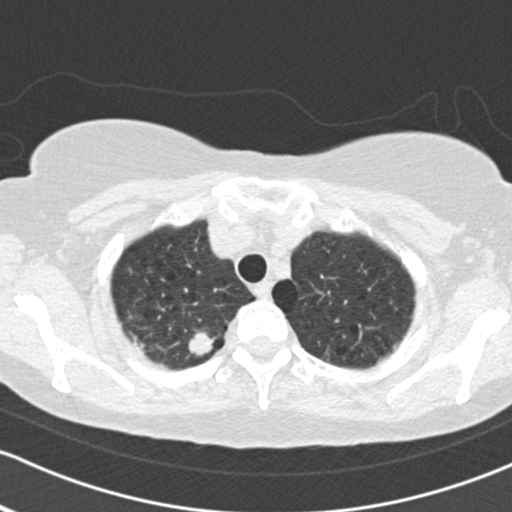
Axial slice from a low-dose chest CT screening exam, second annual screen, lung window (W 1500 / L -600 HU), 2 mm slice thickness, standard (soft-tissue) reconstruction kernel (B30f), slice 20 of 161 in the series. Female participant, aged 64 years at enrolment.
- Expert reader's lesion annotation, bounding box <172,322,224,370> (left, top, right, bottom; pixels).
- Screening reader's record for this exam (one nodule recorded; not confirmed to be the boxed lesion): non-calcified nodule or mass ≥4 mm, right upper lobe, 16 × 15 mm, spiculated (stellate) margins, soft tissue attenuation, pre-existing on the prior screen: no.
- Lung cancer was diagnosed 45 days after this screen: adenocarcinoma, NOS, right upper lobe, poorly differentiated (G3), stage IB (AJCC 6th edition), 15 mm at pathology.